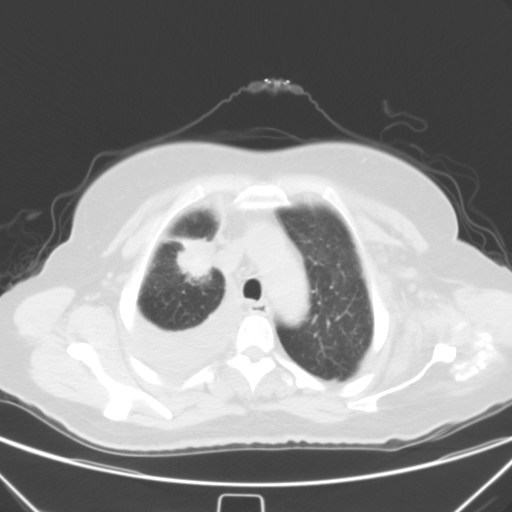
Chest CT, one axial slice. Position 45 of 55 along the scan axis. 120 kVp. Lung window (W 1500 / L -600 HU). 512 × 512 image matrix, field of view 352 × 352 mm. Female patient, age 66 years. Case-level facts recorded for this patient, not image findings: clinical TNM (as recorded): T2 N0 M1.
Annotated regions visible in this slice (rectangle marked by the reading radiologist):
- lung tumour (recorded histology: adenocarcinoma): bounding box [x1, y1, x2, y2] px = [172, 236, 217, 277]